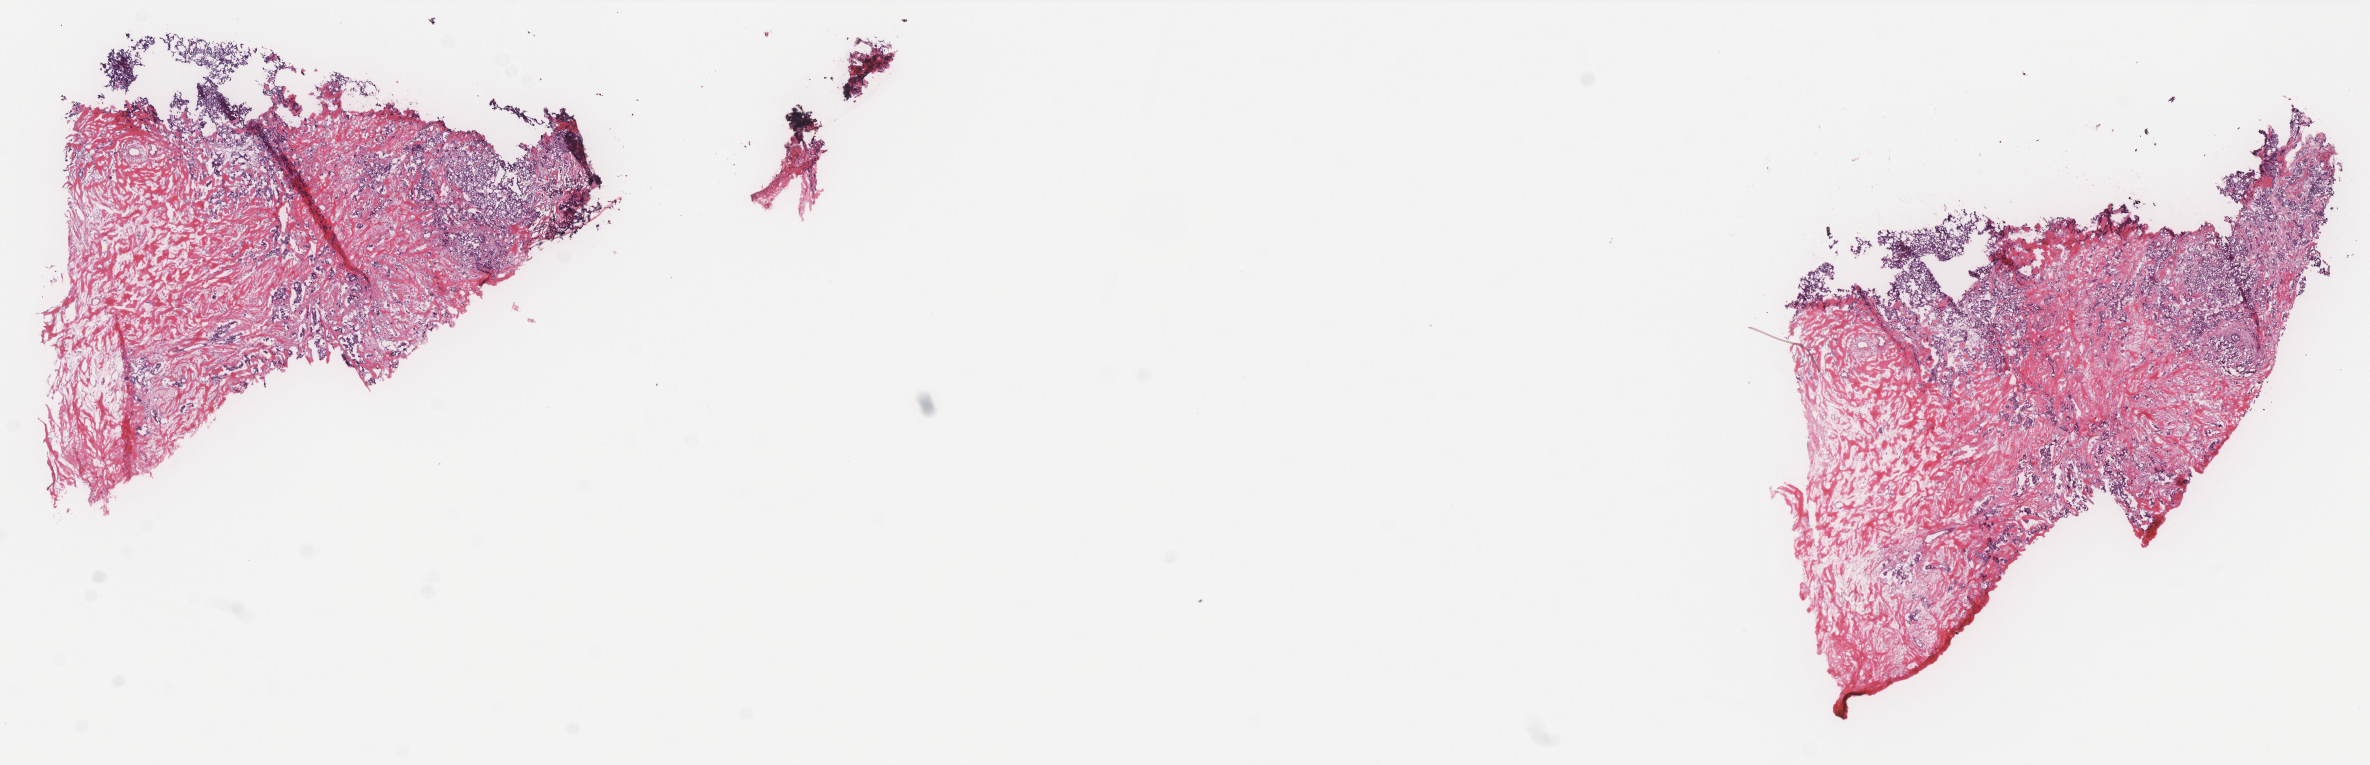
H&E-stained whole-slide image — low-resolution overview of the scanned area, about 19.0 x 6.1 mm, frozen section from the top of the tissue portion, primary tumour sample from the breast. Female patient; age at initial diagnosis 58 years. Pathologist review of this section (percent, as recorded): tumour cells 75%, tumour nuclei 75%, normal cells 2%, stromal cells 23%, necrosis 0%. Infiltration values recorded for this section: lymphocyte infiltration 2%, monocyte infiltration 0%, neutrophil infiltration 0%.
• laterality: right
• histologic diagnosis: Infiltrating duct carcinoma, NOS
• lymph nodes positive (case pathology): 5 of 18 examined